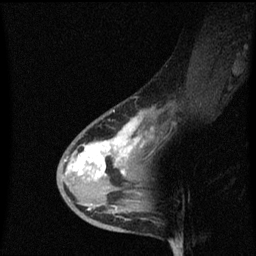
Breast MRI (dynamic contrast-enhanced), one sagittal slice; position 31 of 60 along the scan axis; dynamic contrast-enhanced series, image 2 of 3 at this slice position (ordered by acquisition); 1.5 T; TE 4.2 ms, TR 8.4 ms; 256 × 256 image matrix, field of view 200 × 200 mm. Female patient, age 38 years. From the clinical record (not read from this slice): setting: breast cancer imaged before/during neoadjuvant chemotherapy; receptor status: HR-positive, HER2-negative.
Structures marked on this image (semi-automatically segmented with operator editing):
- analysis volume of interest (the breast-tissue region the enhancement analysis was run in; not a lesion): bounding box [x1, y1, x2, y2] px = [58, 106, 151, 205]
- tumour enhancement mask (voxels above the 70 % enhancement threshold inside the analysis volume of interest): [64, 116, 143, 177]